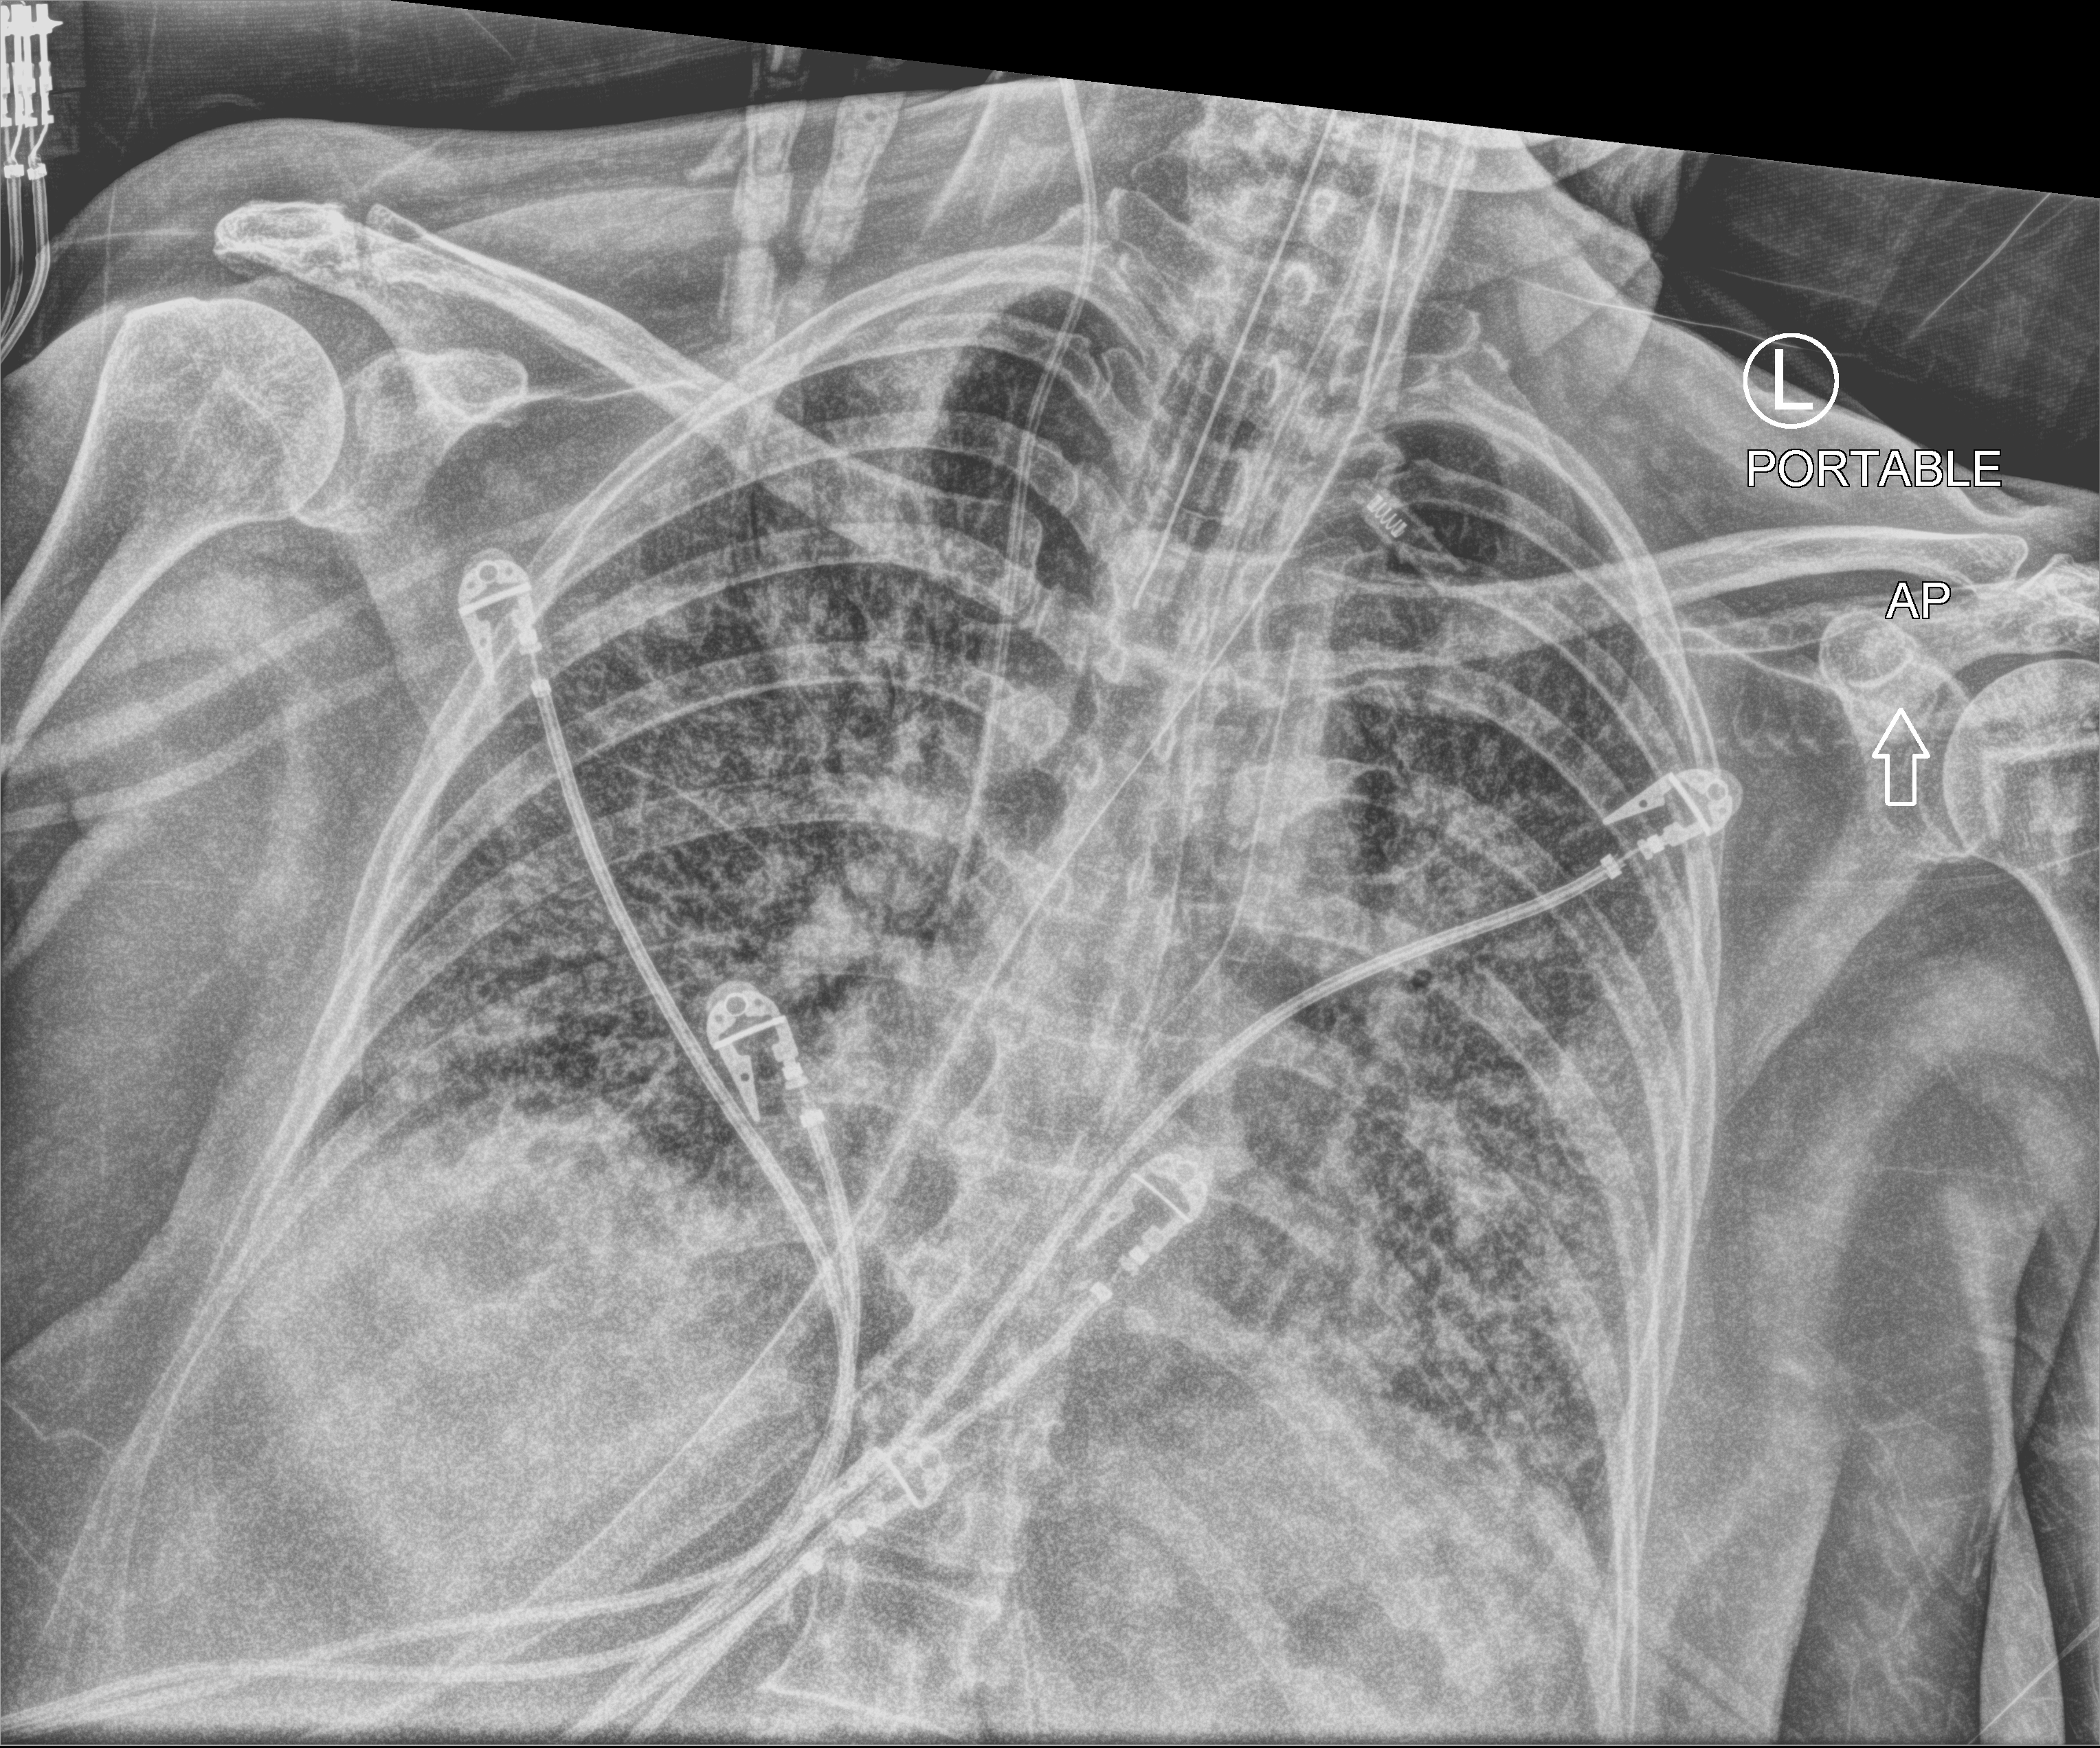
Bedside chest radiograph (computed radiography), anteroposterior (AP) projection. Patient hospitalised with COVID-19; female, aged 60–74 years.
From the hospital-stay record, not from the radiograph (when in the stay this image was taken is not recorded):
- mechanically ventilated during this hospital stay: yes